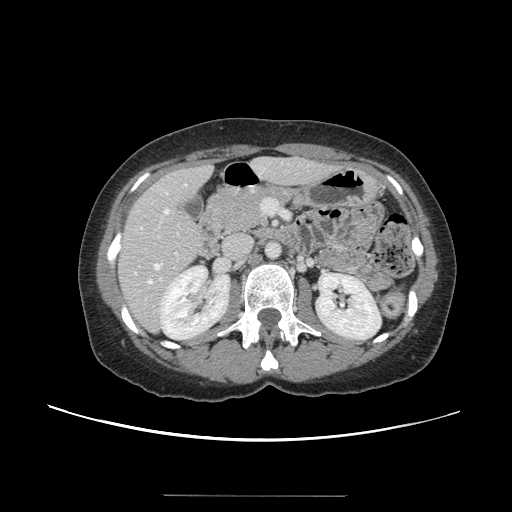
Contrast-enhanced abdominal CT, one axial slice; slice 64 of 144 in the series (ordered by position); 120 kVp; intravenous contrast given; soft-tissue window (W 400 / L 40 HU); 2.5 mm slice thickness; 512 × 512 image matrix, field of view 380 × 380 mm. Female patient, age 53 years. Case-level facts recorded for this patient, not image findings: diagnosis: colorectal cancer liver metastases, imaged before liver resection; multiple liver metastases: yes; largest metastasis: 1.1 cm; chemotherapy before resection: no.
Outlined on this slice (expert manual segmentation):
- hepatic veins: bounding box (x1, y1, x2, y2) in pixels: (135, 184, 186, 283)
- liver: (120, 159, 334, 331)
- planned liver remnant (the part of the liver to remain after resection): (120, 159, 326, 307)
- portal vein (with intrahepatic branches): (159, 252, 178, 281)